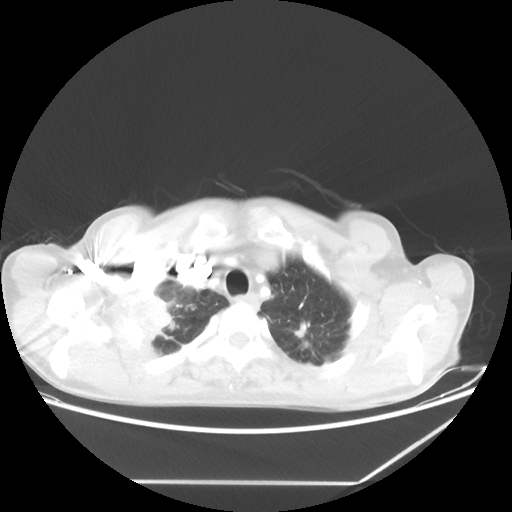
Chest CT, one axial slice; position 57 of 65 along the scan axis; reconstruction kernel STANDARD; lung window (W 1500 / L -600 HU); 5 mm slice thickness; 512 × 512 image matrix, field of view 397 × 397 mm. Patient: male, 68 years. Case-level facts recorded for this patient, not image findings: clinical TNM (as recorded): T3 N3 M0.
Outlined on this slice (rectangle marked by the reading radiologist):
- lung tumour (recorded histology: adenocarcinoma): bounding box (x1, y1, x2, y2) in pixels: (125, 286, 187, 350)